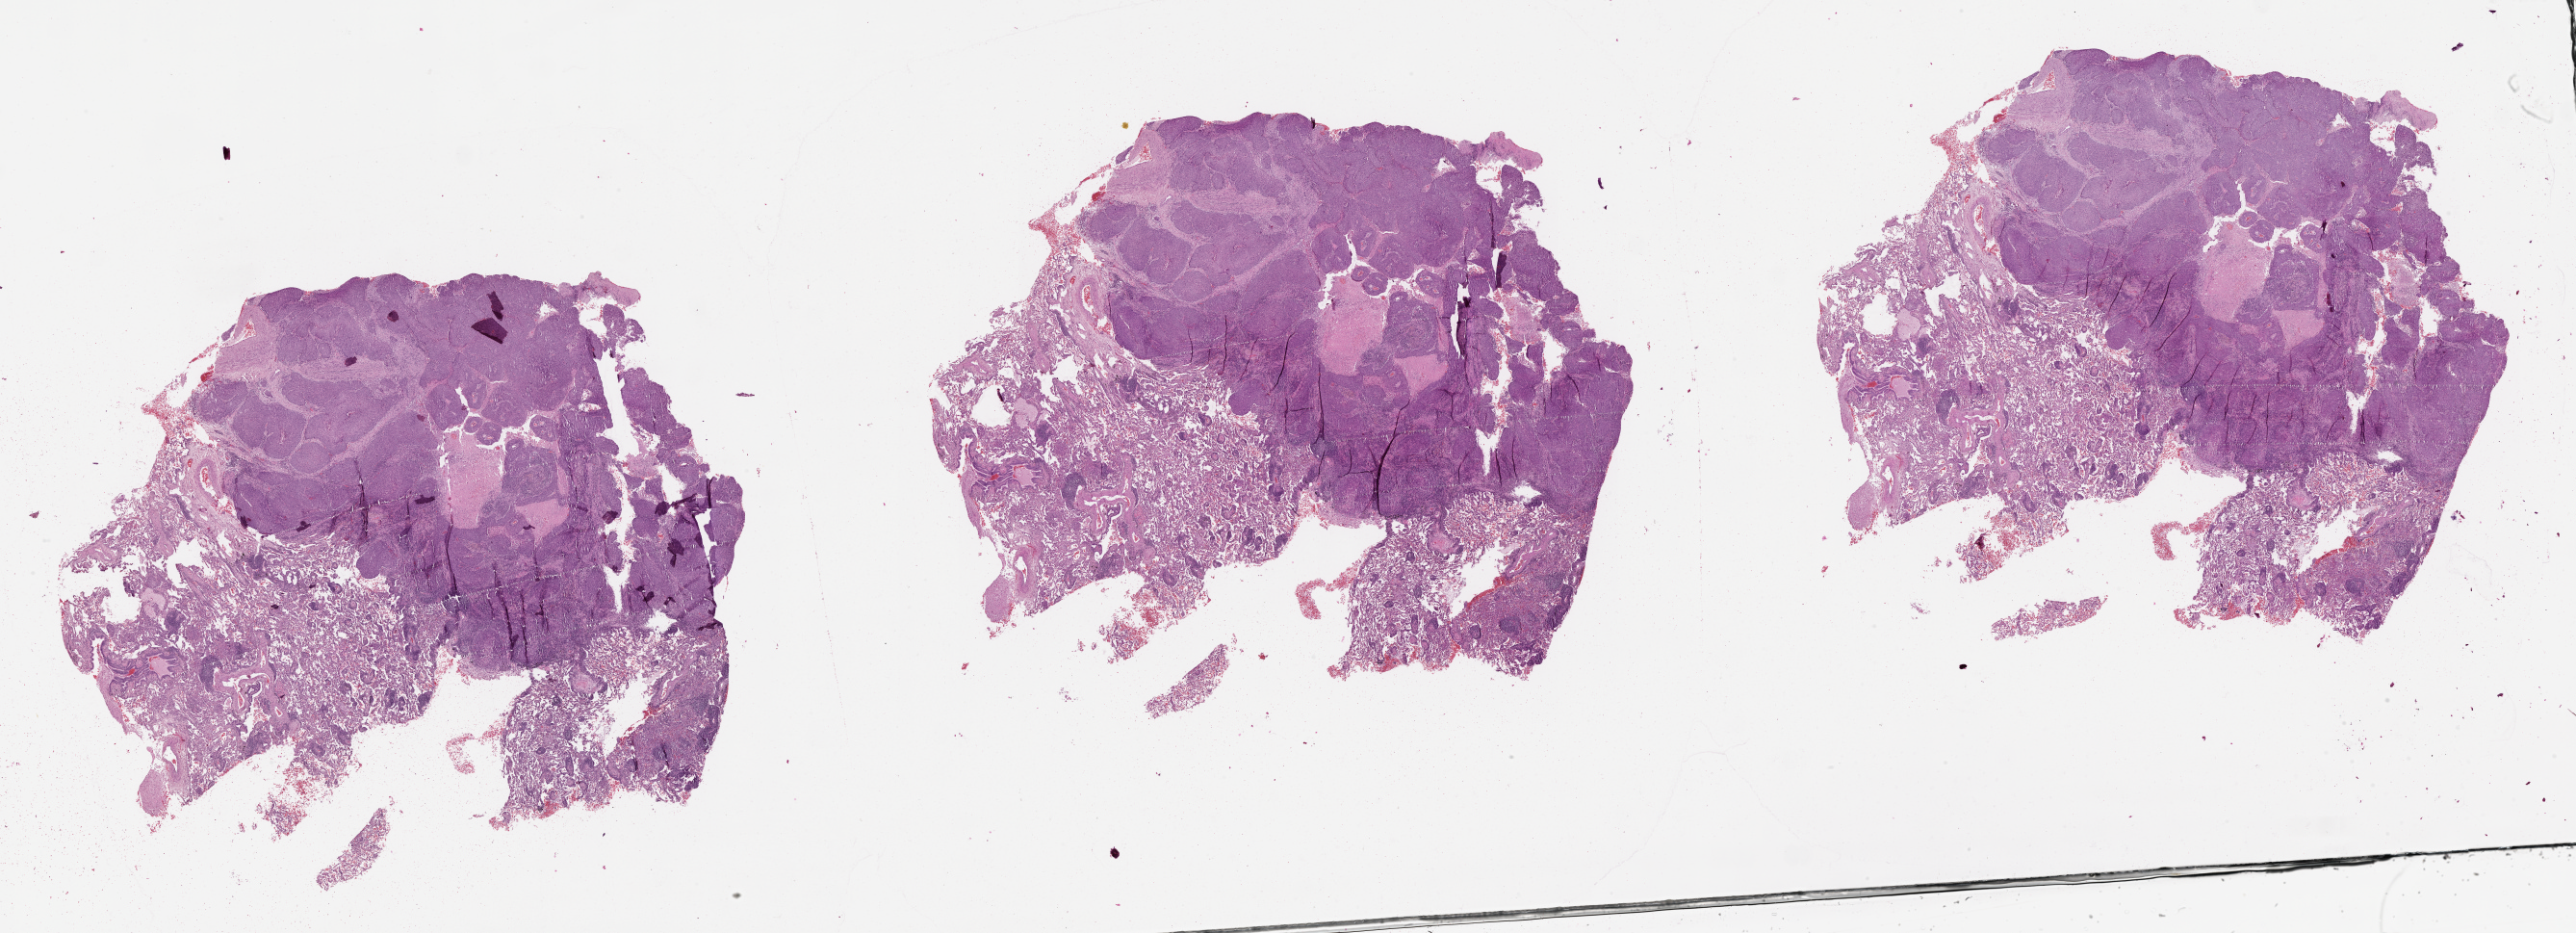
Digitized Hematoxylin and eosin (H&E) stained tissue section (whole slide) — low-resolution overview of the scanned area, about 43.1 x 15.6 mm, tumour tissue sample, lung. Male, 71 y/o.
Patient diagnosis (cohort enrolment): squamous cell carcinoma (lung).